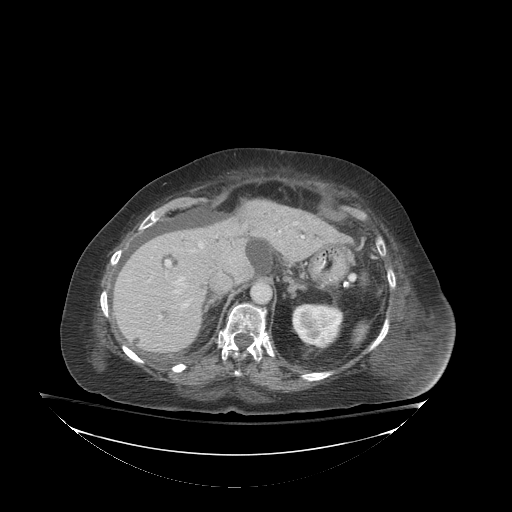
Contrast-enhanced abdominal CT (liver protocol), one axial slice. Slice 58 of 81 in the series (ordered by position). Reconstruction kernel STANDARD. Soft-tissue window (W 400 / L 40 HU). 2.5 mm slice thickness. 512 × 512 image matrix, field of view 500 × 500 mm. From the clinical record (not read from this slice): diagnosis: hepatocellular carcinoma (patient treated with transarterial chemoembolisation; whether this scan precedes or follows treatment is not stated here); TNM stage (as recorded): Stage-I.
Structures marked on this image (semi-automatic segmentation, software-assisted and operator-edited):
- liver parenchyma outside the tumour (the mass and vessels are separate outlines, so this box may not span the whole liver): bounding box [x1, y1, x2, y2] px = [112, 200, 338, 352]
- liver vessels: [166, 236, 304, 307]